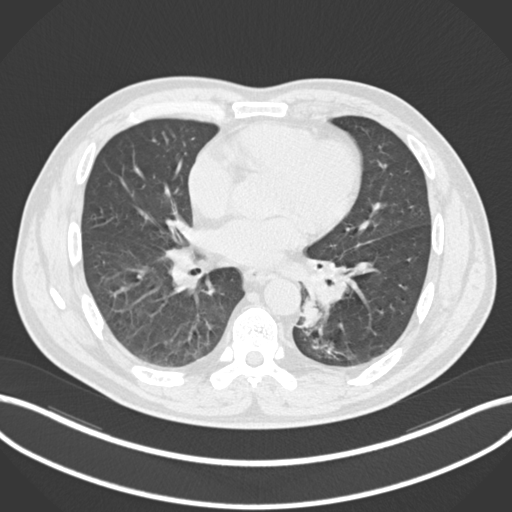
Chest CT, one axial slice. Position 102 of 223 along the scan axis. 120 kVp. Lung window (W 1500 / L -600 HU). 1 mm slice thickness. 512 × 512 image matrix, field of view 400 × 400 mm. Patient: male, 50 years. From the clinical record (not read from this slice): clinical TNM (as recorded): T2a N3 M0.
Annotated regions visible in this slice (rectangle marked by the reading radiologist):
- lung tumour (recorded histology: squamous cell carcinoma): bounding box [x1, y1, x2, y2] px = [296, 292, 326, 332]